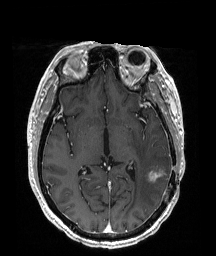
Brain MRI from a brain-tumour surgery series, one axial slice. Position 99 of 192 along the scan axis. T1-weighted post-contrast. 1 mm slice thickness. 216 × 256 image matrix, field of view 211 × 250 mm. From the clinical record (not read from this slice): histopathology: Glioblastoma; WHO grade: 4; IDH mutation: no; tumour location: Left Temporoparietal.
Annotated regions visible in this slice (expert manual segmentation):
- tumour: bounding box (x1, y1, x2, y2) in pixels: (151, 168, 166, 179)